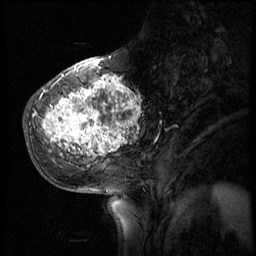
Breast MRI (dynamic contrast-enhanced), one sagittal slice. Position 21 of 56 along the scan axis. 4 images stored at this slice position (order not interpretable as contrast timing). 1.5 T. TE 4.2 ms, TR 8.9 ms. 2.5 mm slice thickness. 256 × 256 image matrix, field of view 220 × 220 mm. Patient: female, 51 years. Case-level facts recorded for this patient, not image findings: setting: breast cancer imaged before/during neoadjuvant chemotherapy; receptor status: triple-negative.
Structures marked on this image (semi-automatically segmented with operator editing):
- analysis volume of interest (the breast-tissue region the enhancement analysis was run in; not a lesion): bounding box <30,70,150,173> (left, top, right, bottom; pixels)
- tumour enhancement mask (voxels above the 140 % enhancement threshold inside the analysis volume of interest): <35,74,142,157>